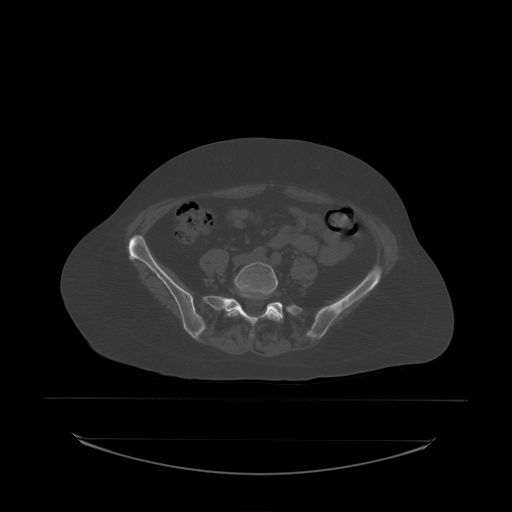
CT including the spine, one axial slice. Slice 35 of 242 in the series (ordered by position). Bone window (W 1800 / L 400 HU). 2.5 mm slice thickness. 512 × 512 image matrix, field of view 500 × 500 mm. Female patient, age 53 years. Case-level facts recorded for this patient, not image findings: primary cancer: lung; vertebrae with lytic lesions (as recorded): T7, L1.
Structures marked on this image (semi-automatically segmented with operator editing):
- L5 vertebra: bounding box [x1, y1, x2, y2] px = [227, 262, 280, 322]